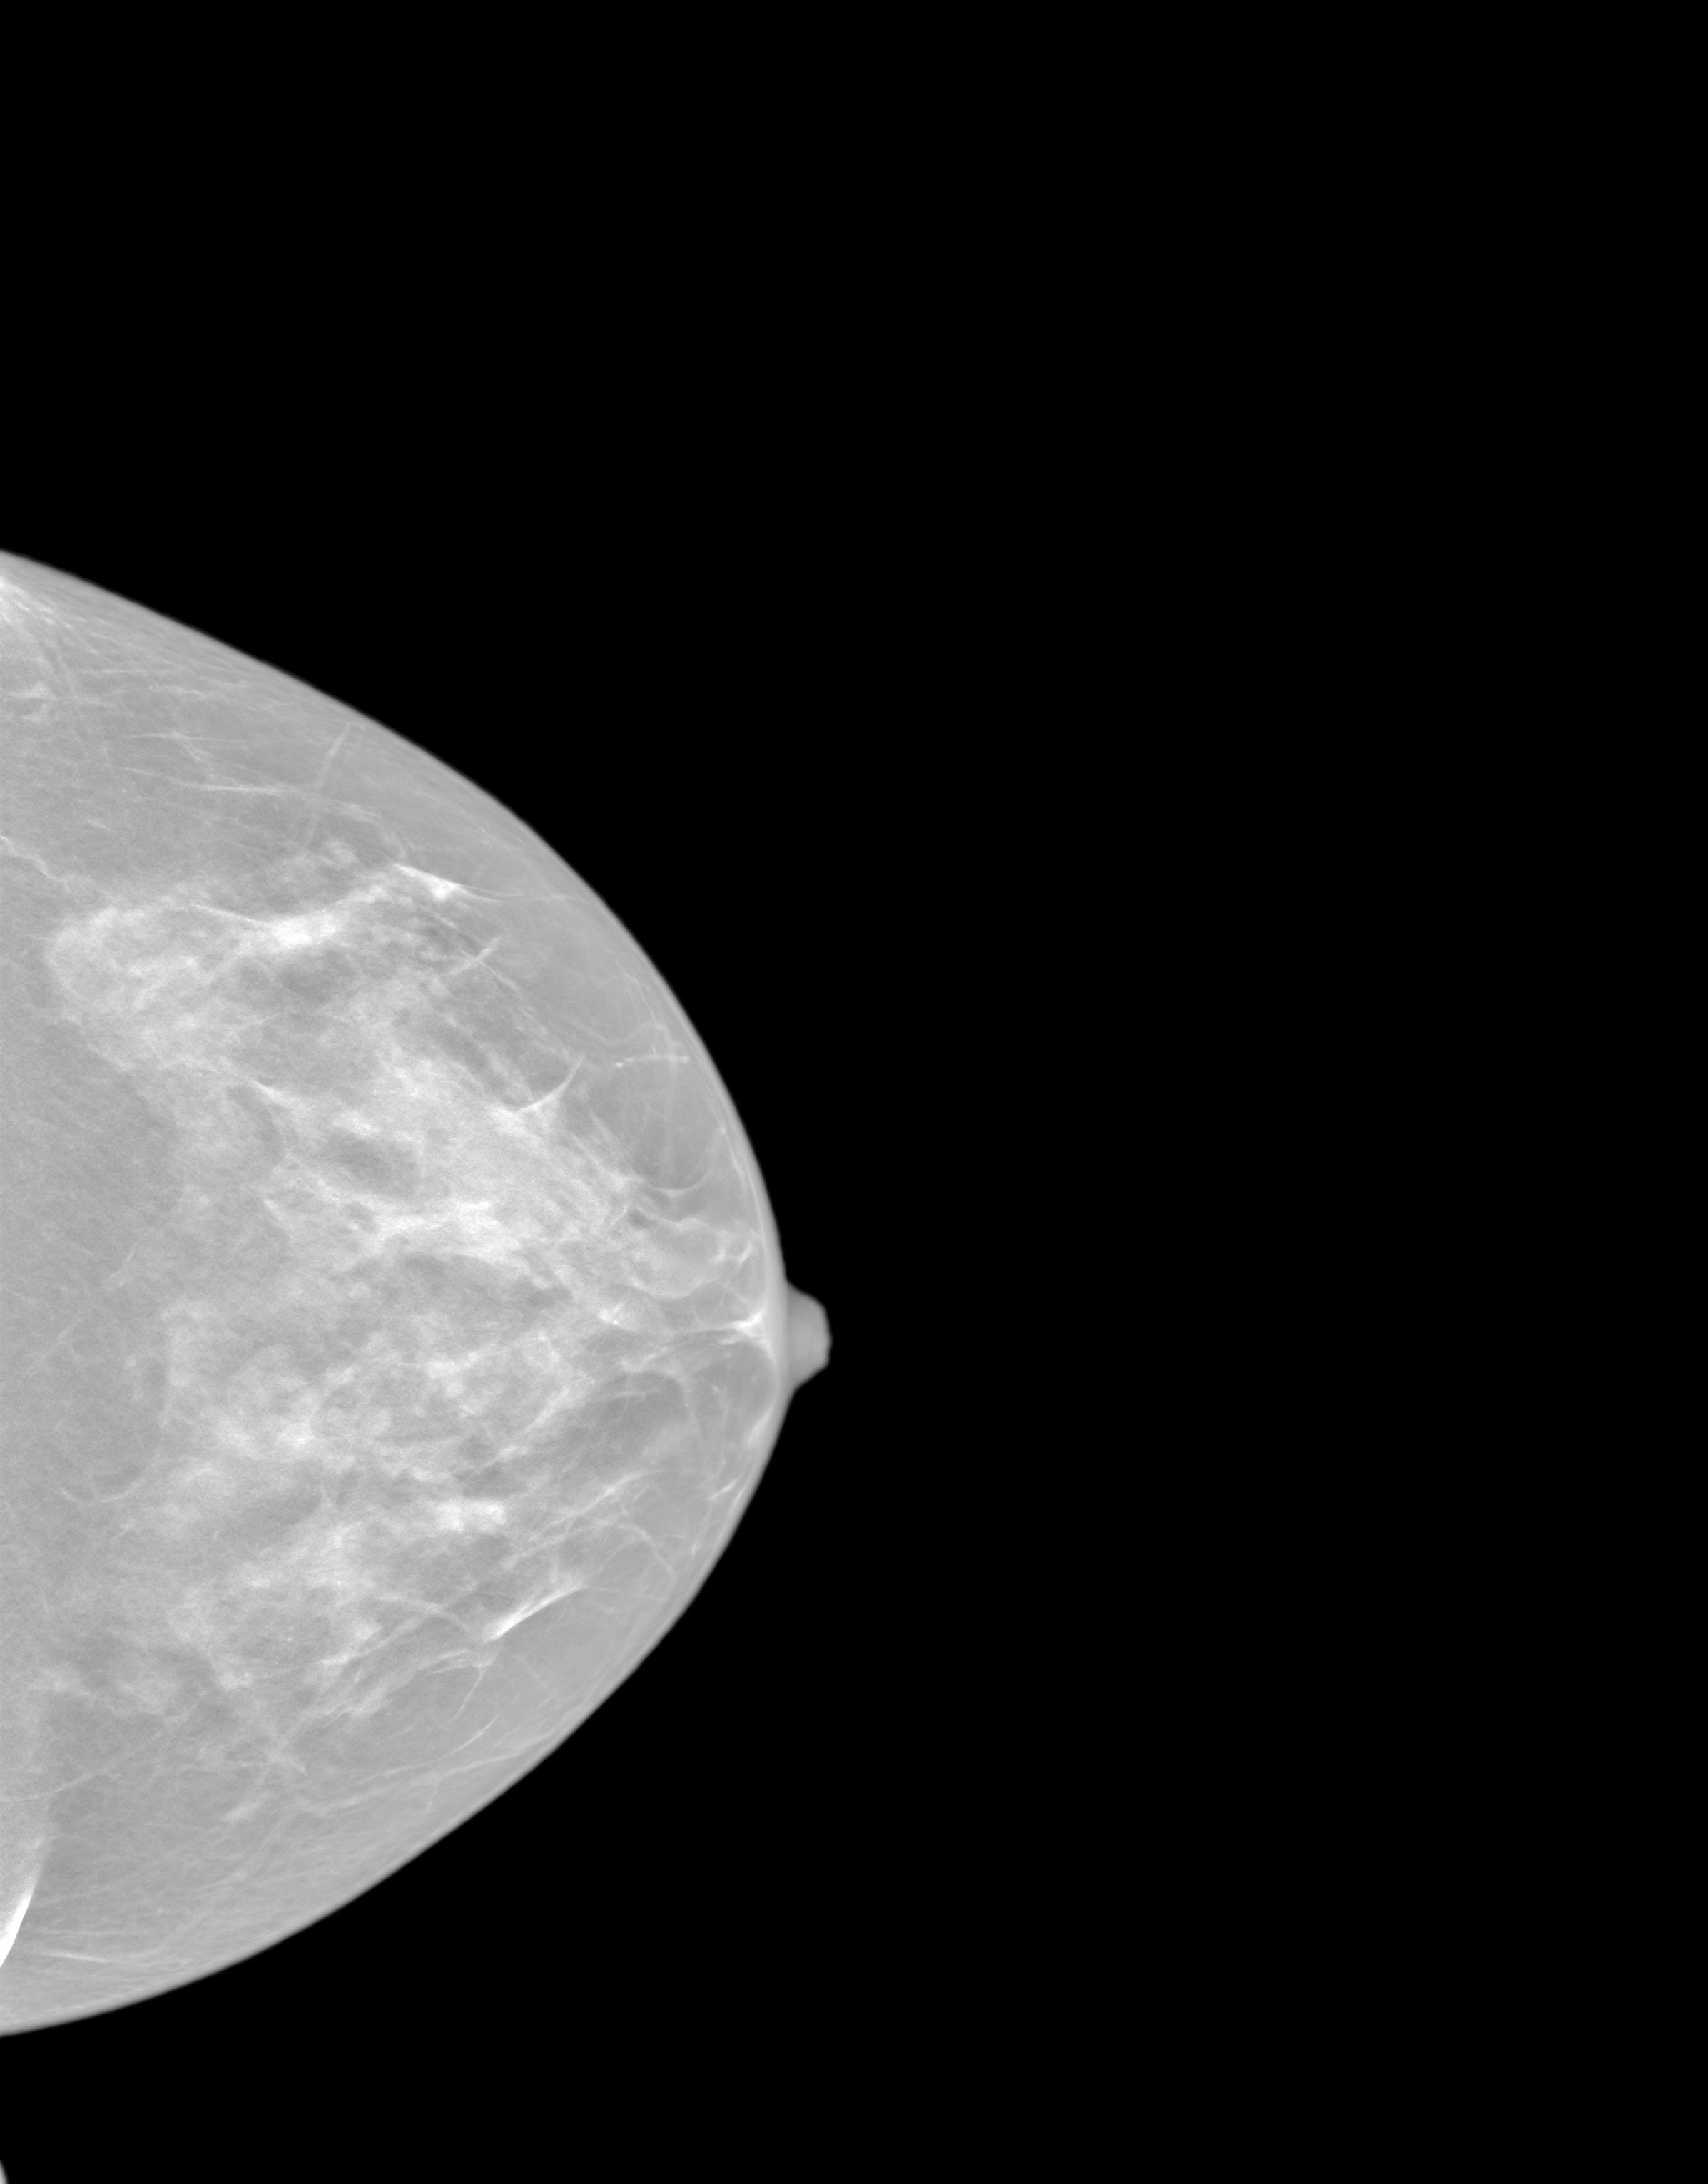
Annual screening mammography examination. Female patient, age 46 years.
Image type: synthesized 2-D view from tomosynthesis. Breast: left. Projection: cranio-caudal projection.